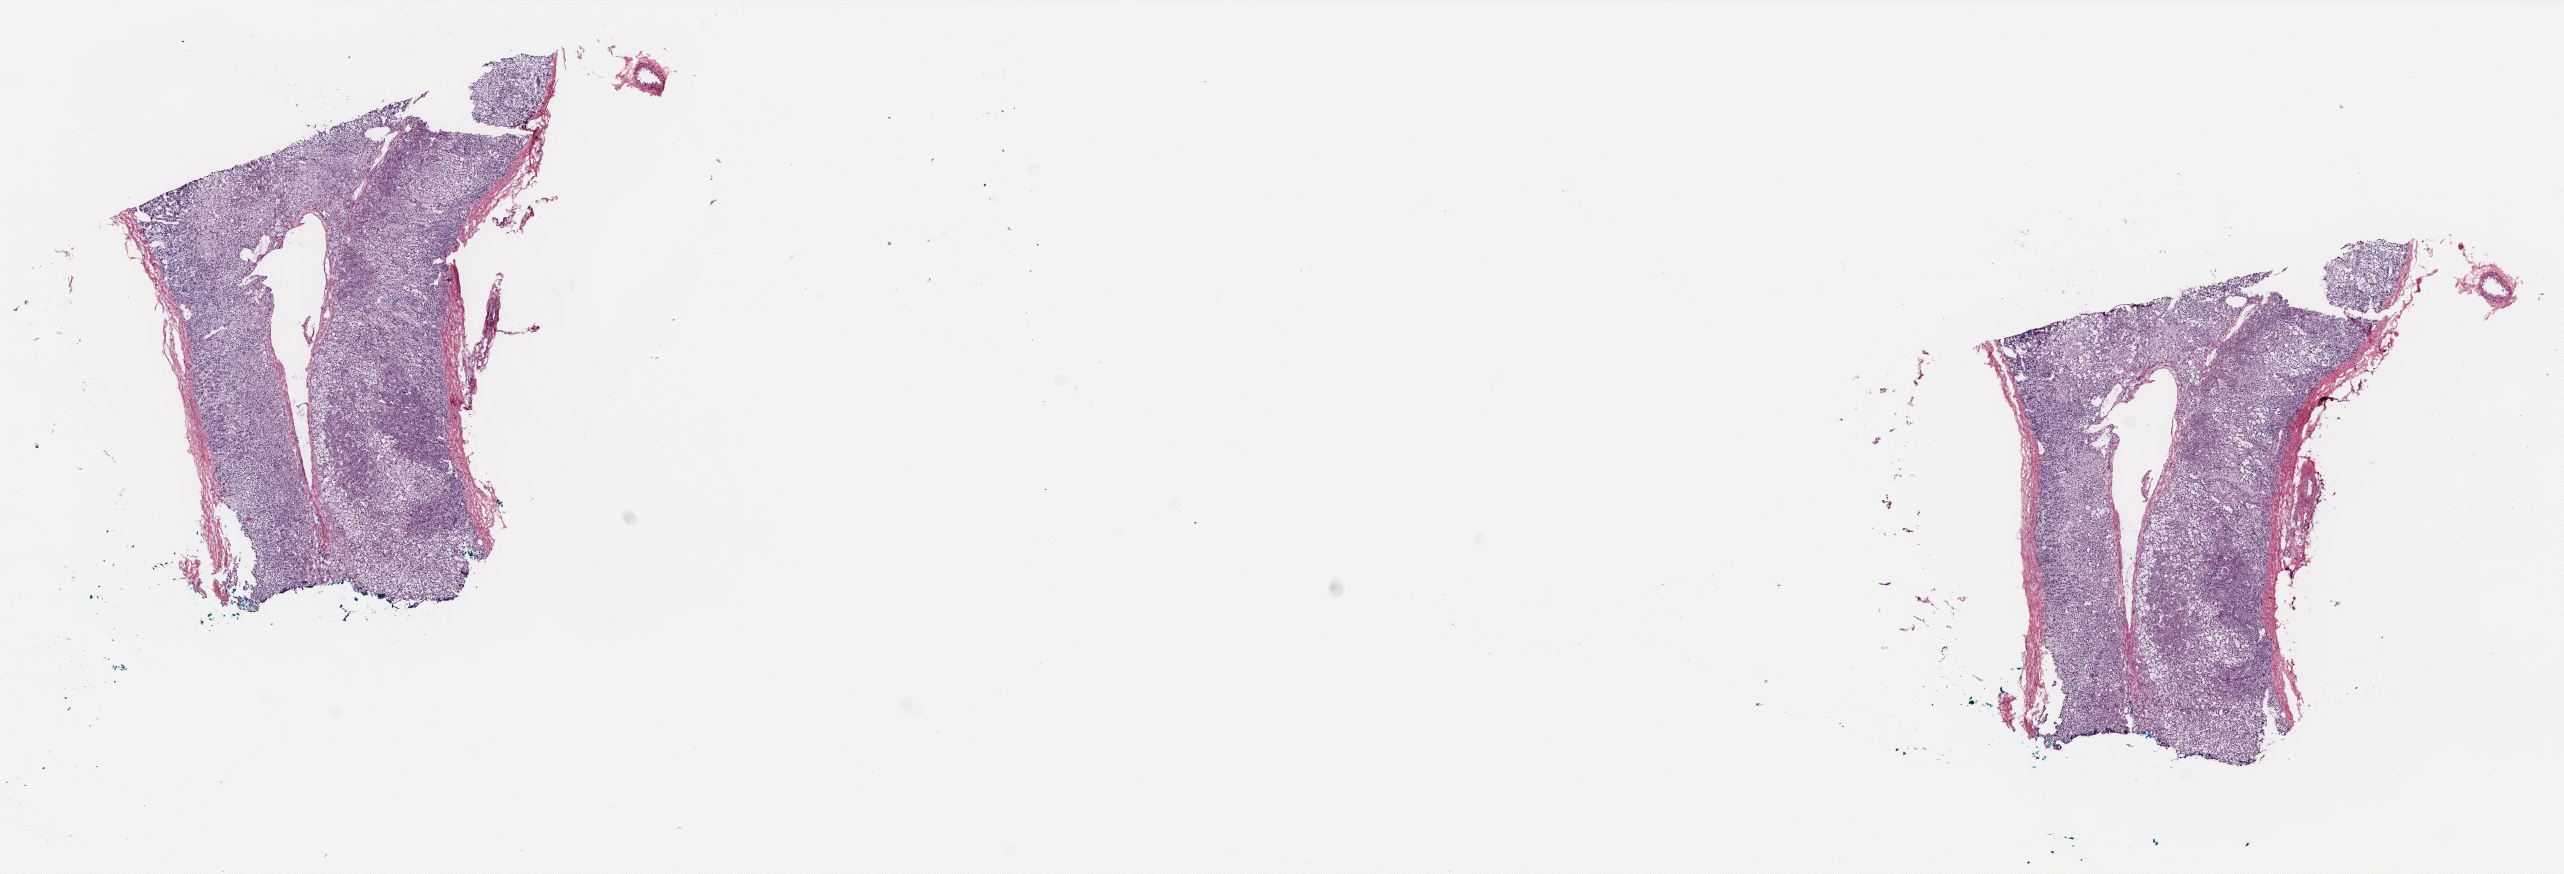
Whole-slide histology image, Hematoxylin and eosin (H&E) stained — whole scanned area (about 20.7 x 7.1 mm) shown as a low-resolution overview. Frozen section from the top of the tissue portion. Solid tissue normal (non-tumour tissue) sample from the adrenal gland. Male patient; age at initial diagnosis 53 years. Composition of this section per pathologist review: tumour cells 0%, tumour nuclei 0%, normal cells 100%, stromal cells 0%, necrosis 0%. Inflammatory infiltration, as recorded: lymphocyte infiltration 1%, monocyte infiltration 0%, neutrophil infiltration 0%.
This section: solid tissue normal (non-tumour) sample from the same patient. Patient diagnosis: Pheochromocytoma, NOS.